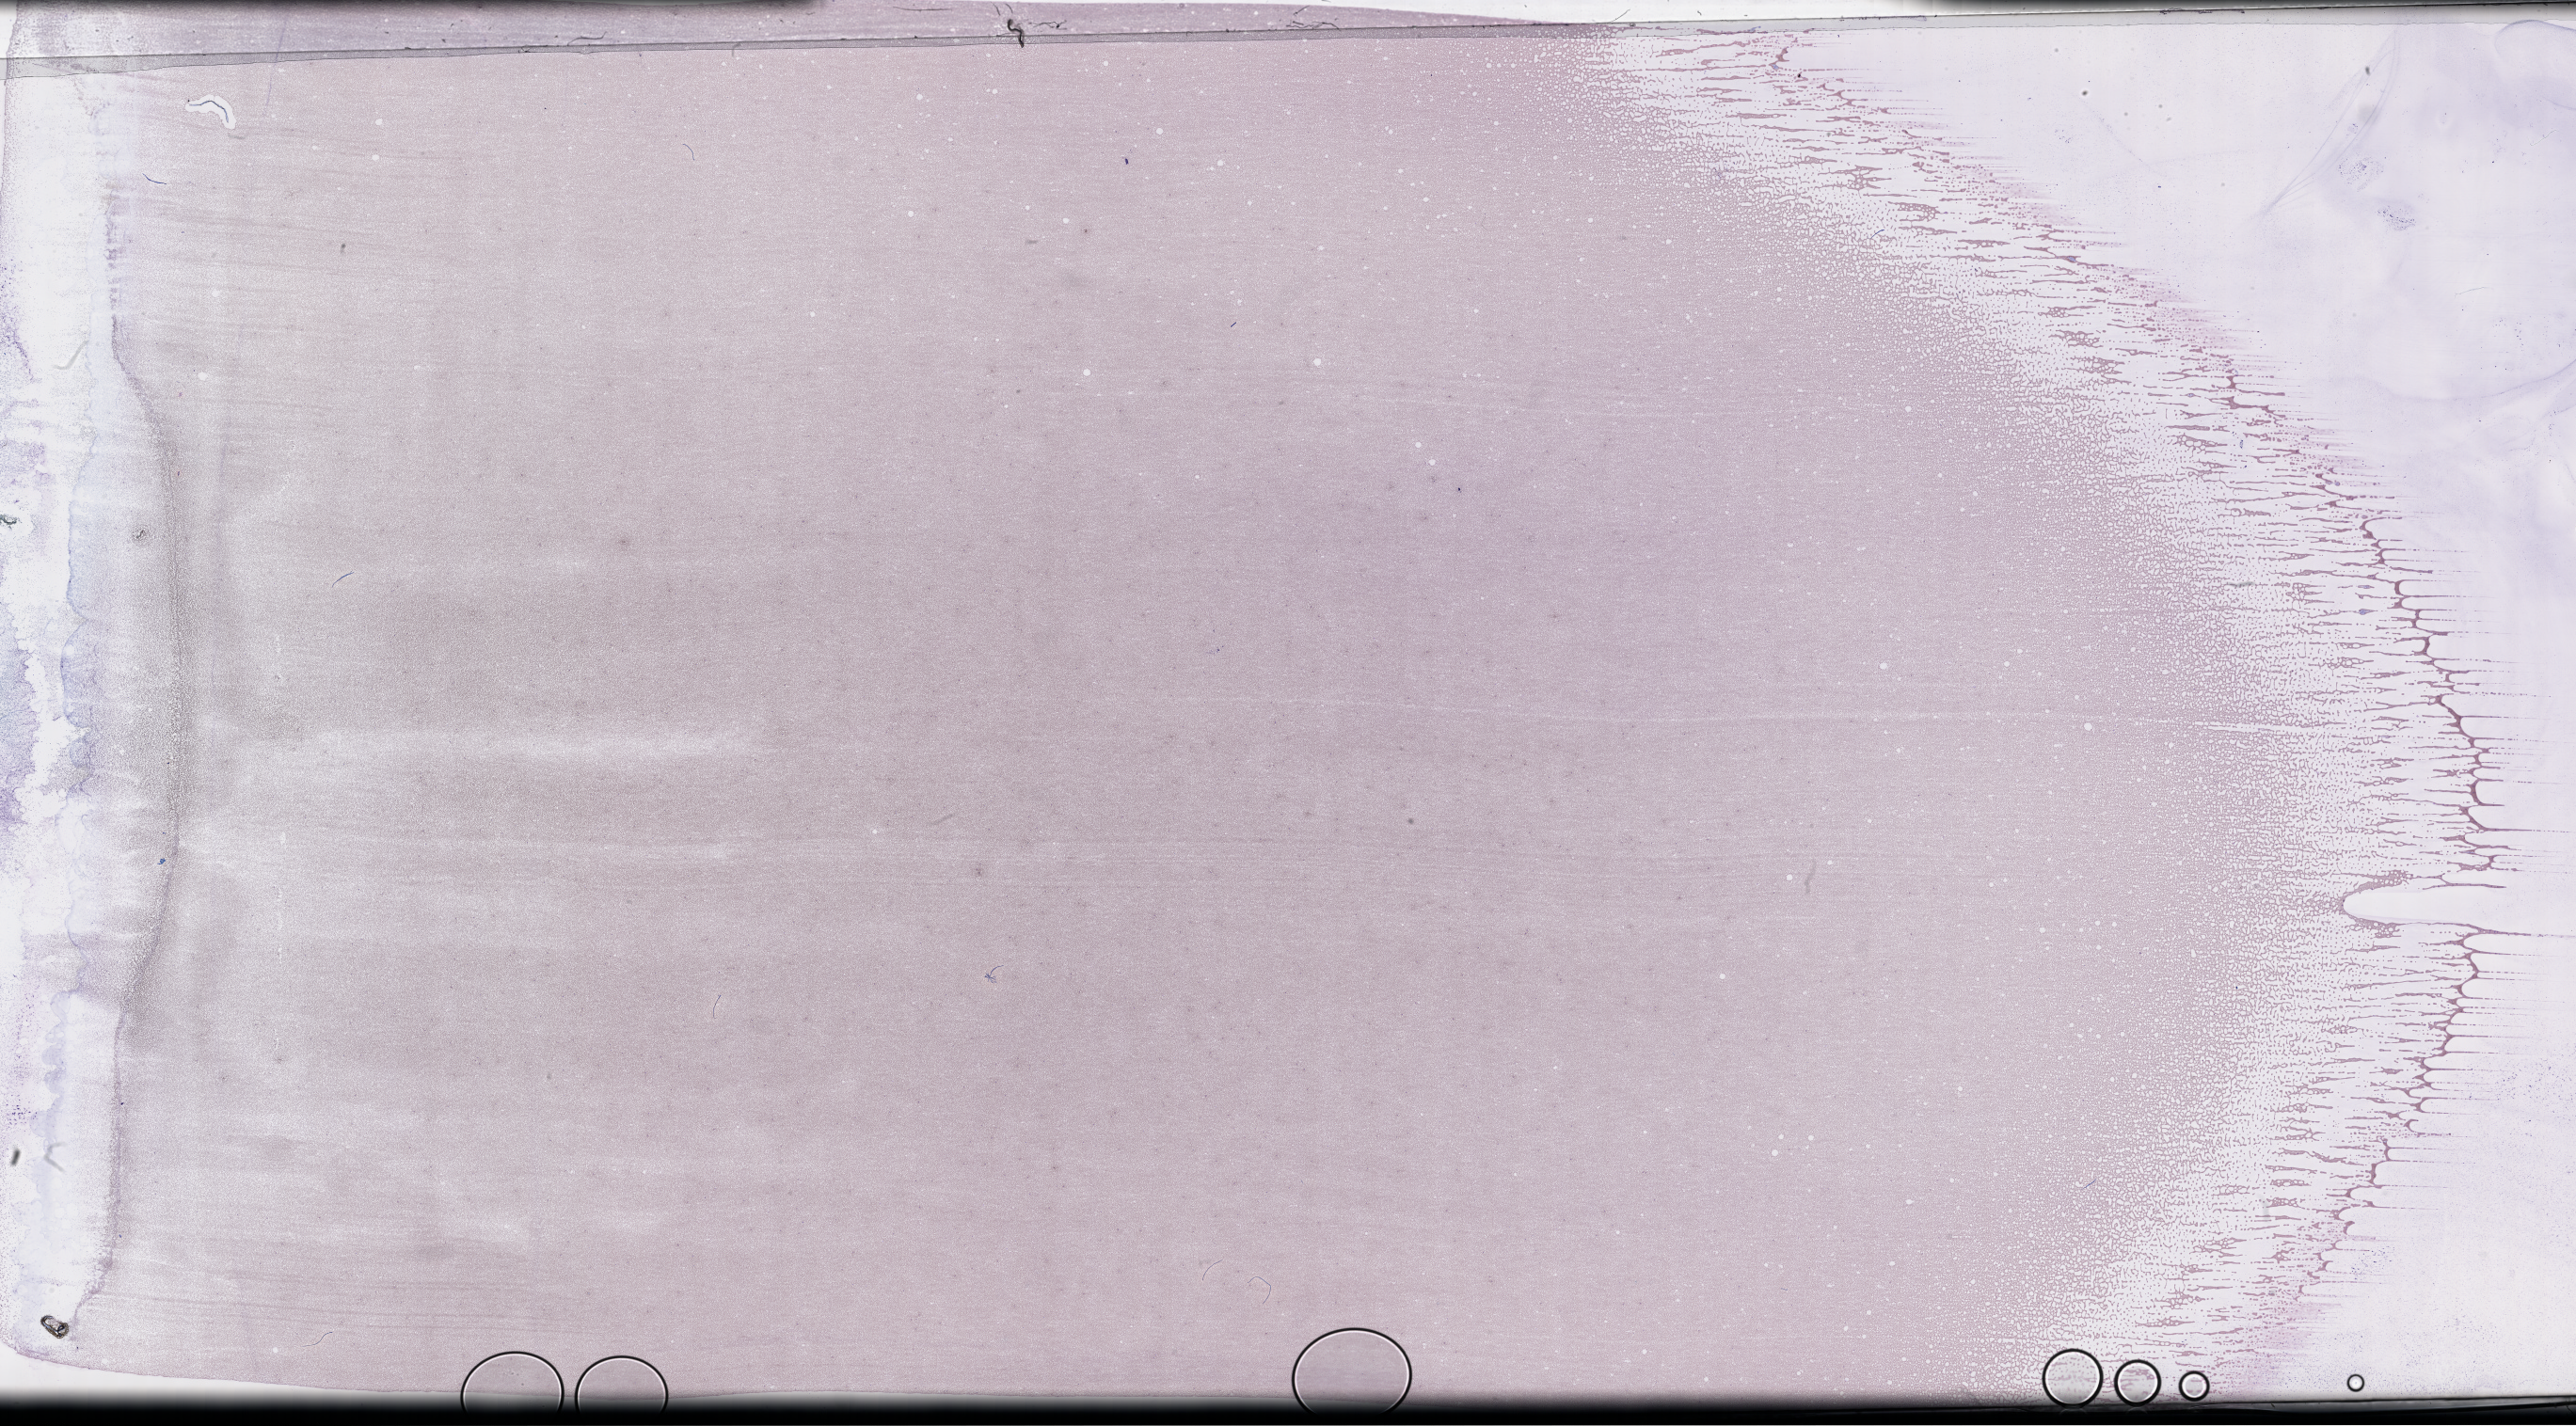
Wright–Giemsa-stained whole blood smear, whole-slide image, low-resolution overview of the scanned area, about 44.2 x 24.5 mm; EDTA-anticoagulated smear. Patient sex: female.
Patient diagnosis: Plasma Cell Myeloma.